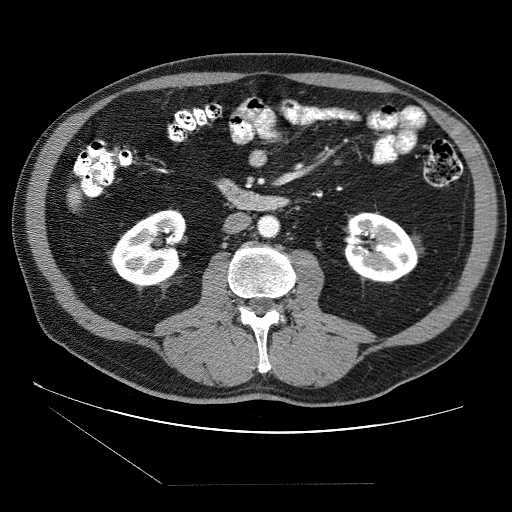
Contrast-enhanced abdominal CT (liver protocol), one axial slice. Position 4 of 87 along the scan axis. Soft-tissue window (W 400 / L 40 HU). 512 × 512 image matrix, field of view 400 × 400 mm. From the clinical record (not read from this slice): diagnosis: hepatocellular carcinoma (patient treated with transarterial chemoembolisation; whether this scan precedes or follows treatment is not stated here); TNM stage (as recorded): Stage-II; Child-Pugh class: B; tumour differentiation: no biopsy.
Structures marked on this image (semi-automatically segmented with operator editing):
- liver parenchyma outside the tumour (the mass and vessels are separate outlines, so this box may not span the whole liver): bounding box [x1, y1, x2, y2] px = [68, 187, 78, 208]